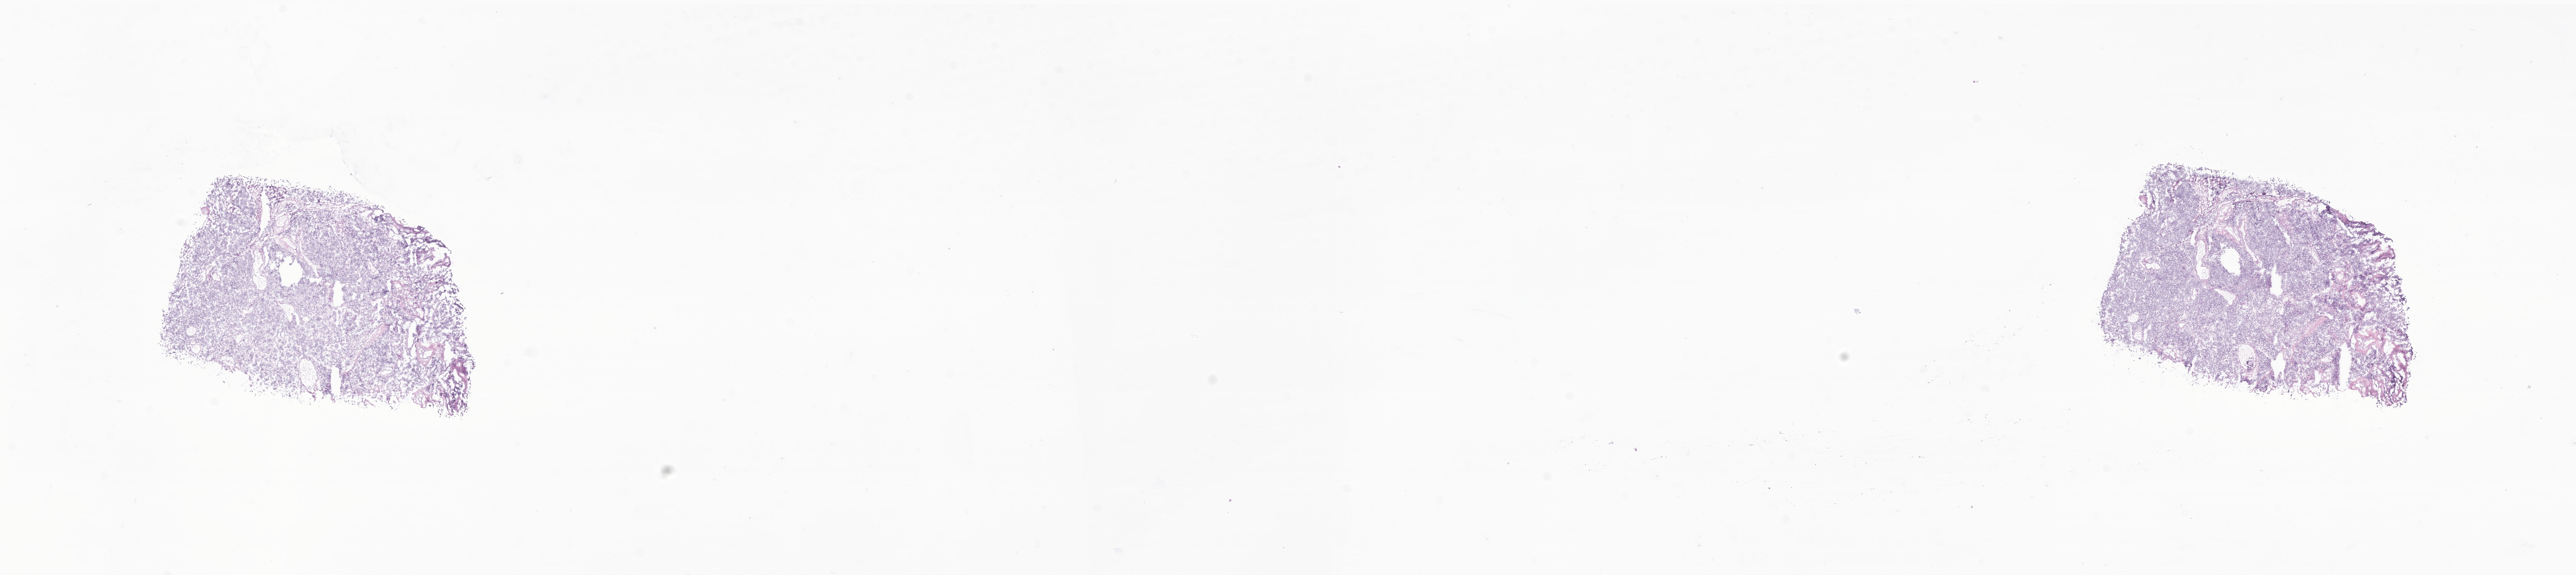
Digitized H&E-stained section of tumor tissue from the brain — shown as a low-resolution overview of the whole scanned area (about 29.4 x 6.6 mm), frozen section. Male patient, age 173 months (14 years 5 months).
* recorded diagnosis: Medulloblastoma, NOS